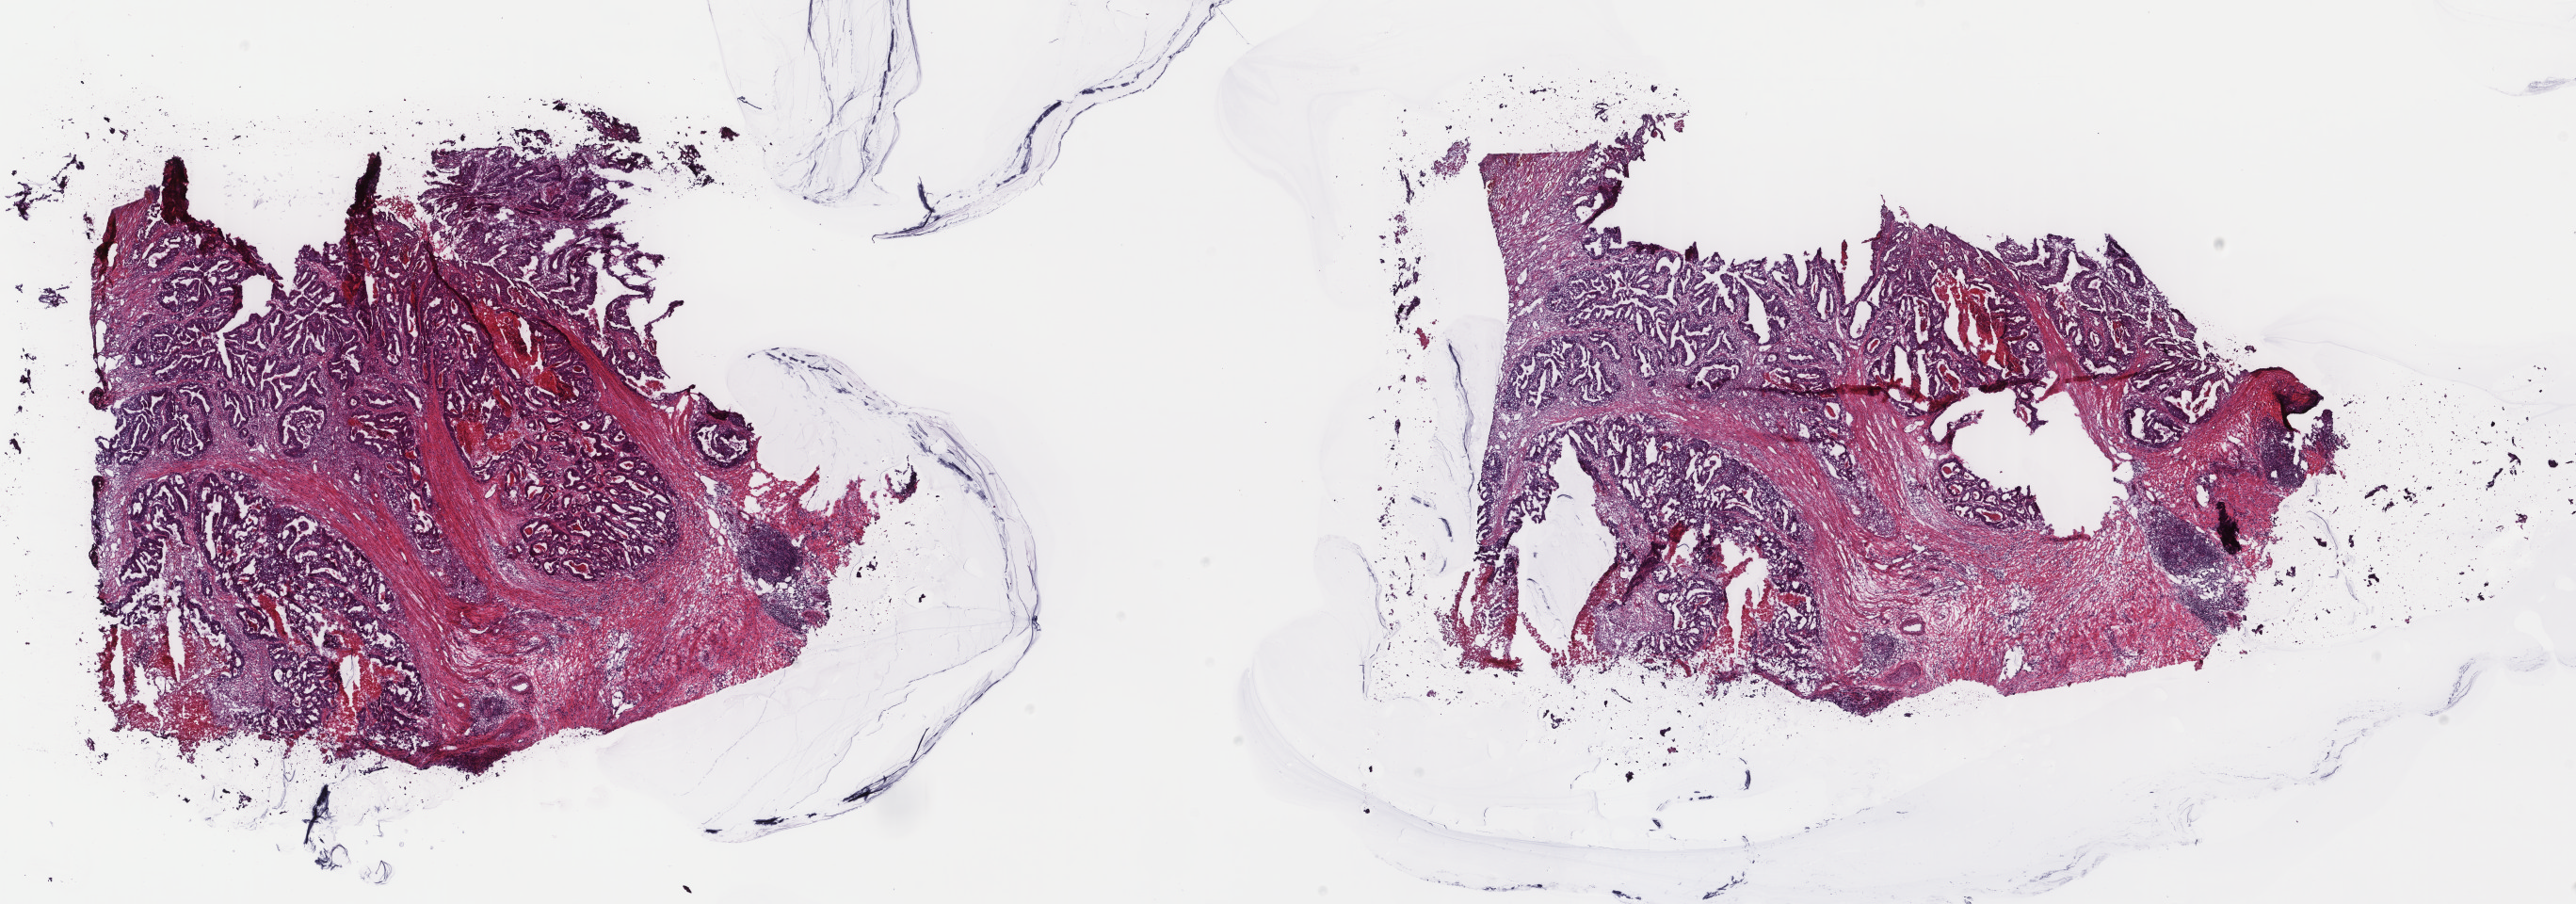
Digitized H&E tissue section (whole slide), a low-resolution overview of the entire scanned area, about 21.7 x 7.6 mm, frozen section from the top of the tissue portion, sample: primary tumour, rectum. Female patient; age at initial diagnosis 56 years. Pathologist review of this section (percent, as recorded): tumour cells 75%, tumour nuclei 60%, normal cells 0%, stromal cells 20%, necrosis 5%. Infiltration values recorded for this section: lymphocyte infiltration 0%, monocyte infiltration 0%, neutrophil infiltration 0%.
- pathologic diagnosis: Adenocarcinoma, NOS
- lymph nodes positive (case pathology): 0 of 14 examined
- AJCC pathologic stage: IIA